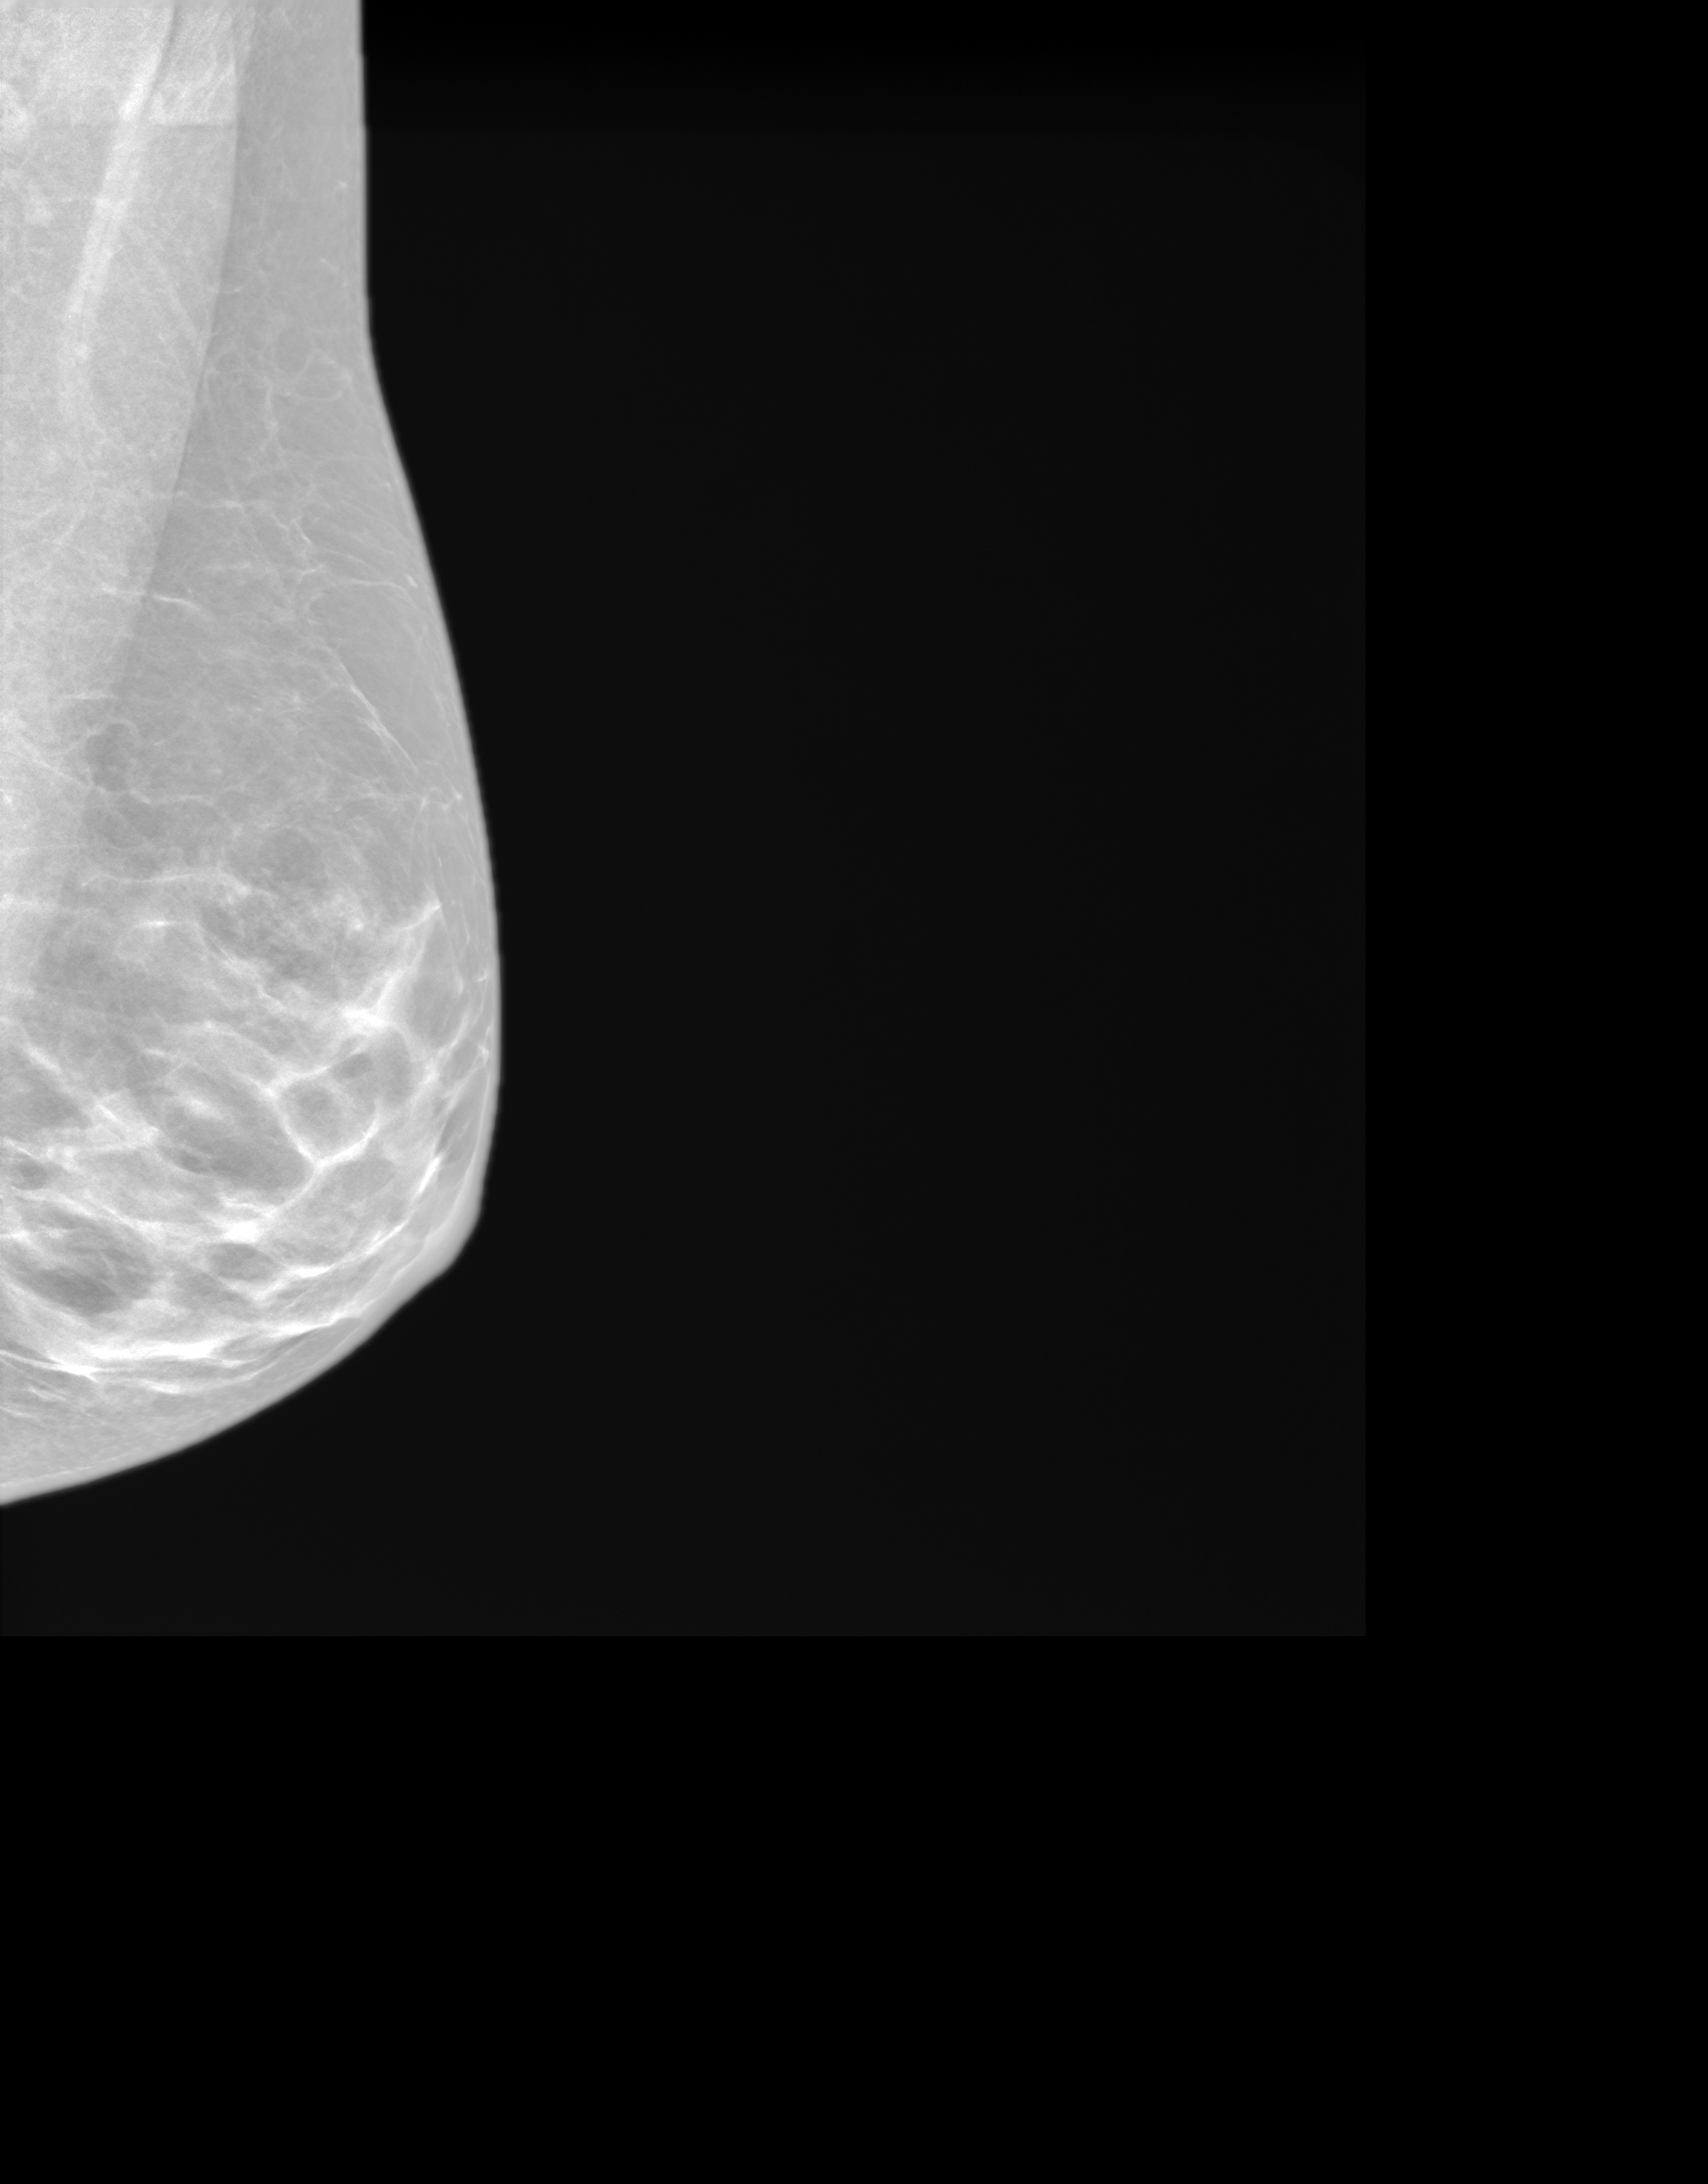
Screening examination. Female patient, age 67 years.
Image type: synthesized 2-D view from tomosynthesis. Breast: left. Projection: MLO view.